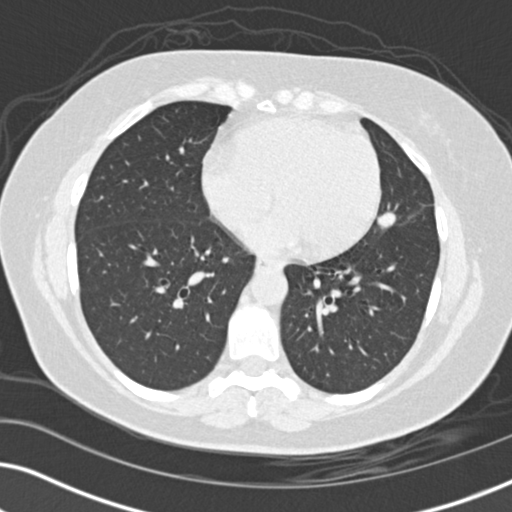
Low-dose screening chest CT, one axial slice. Slice 66 of 152 in the series (ordered by position). Reconstruction kernel B30f. 120 kVp. Lung window (W 1500 / L -600 HU). 512 × 512 image matrix.
Annotated regions visible in this slice (manually delineated by an expert):
- lesion 1 (tumor, upper lobe of left lung): box from (x=377, y=212) to (x=396, y=227) px